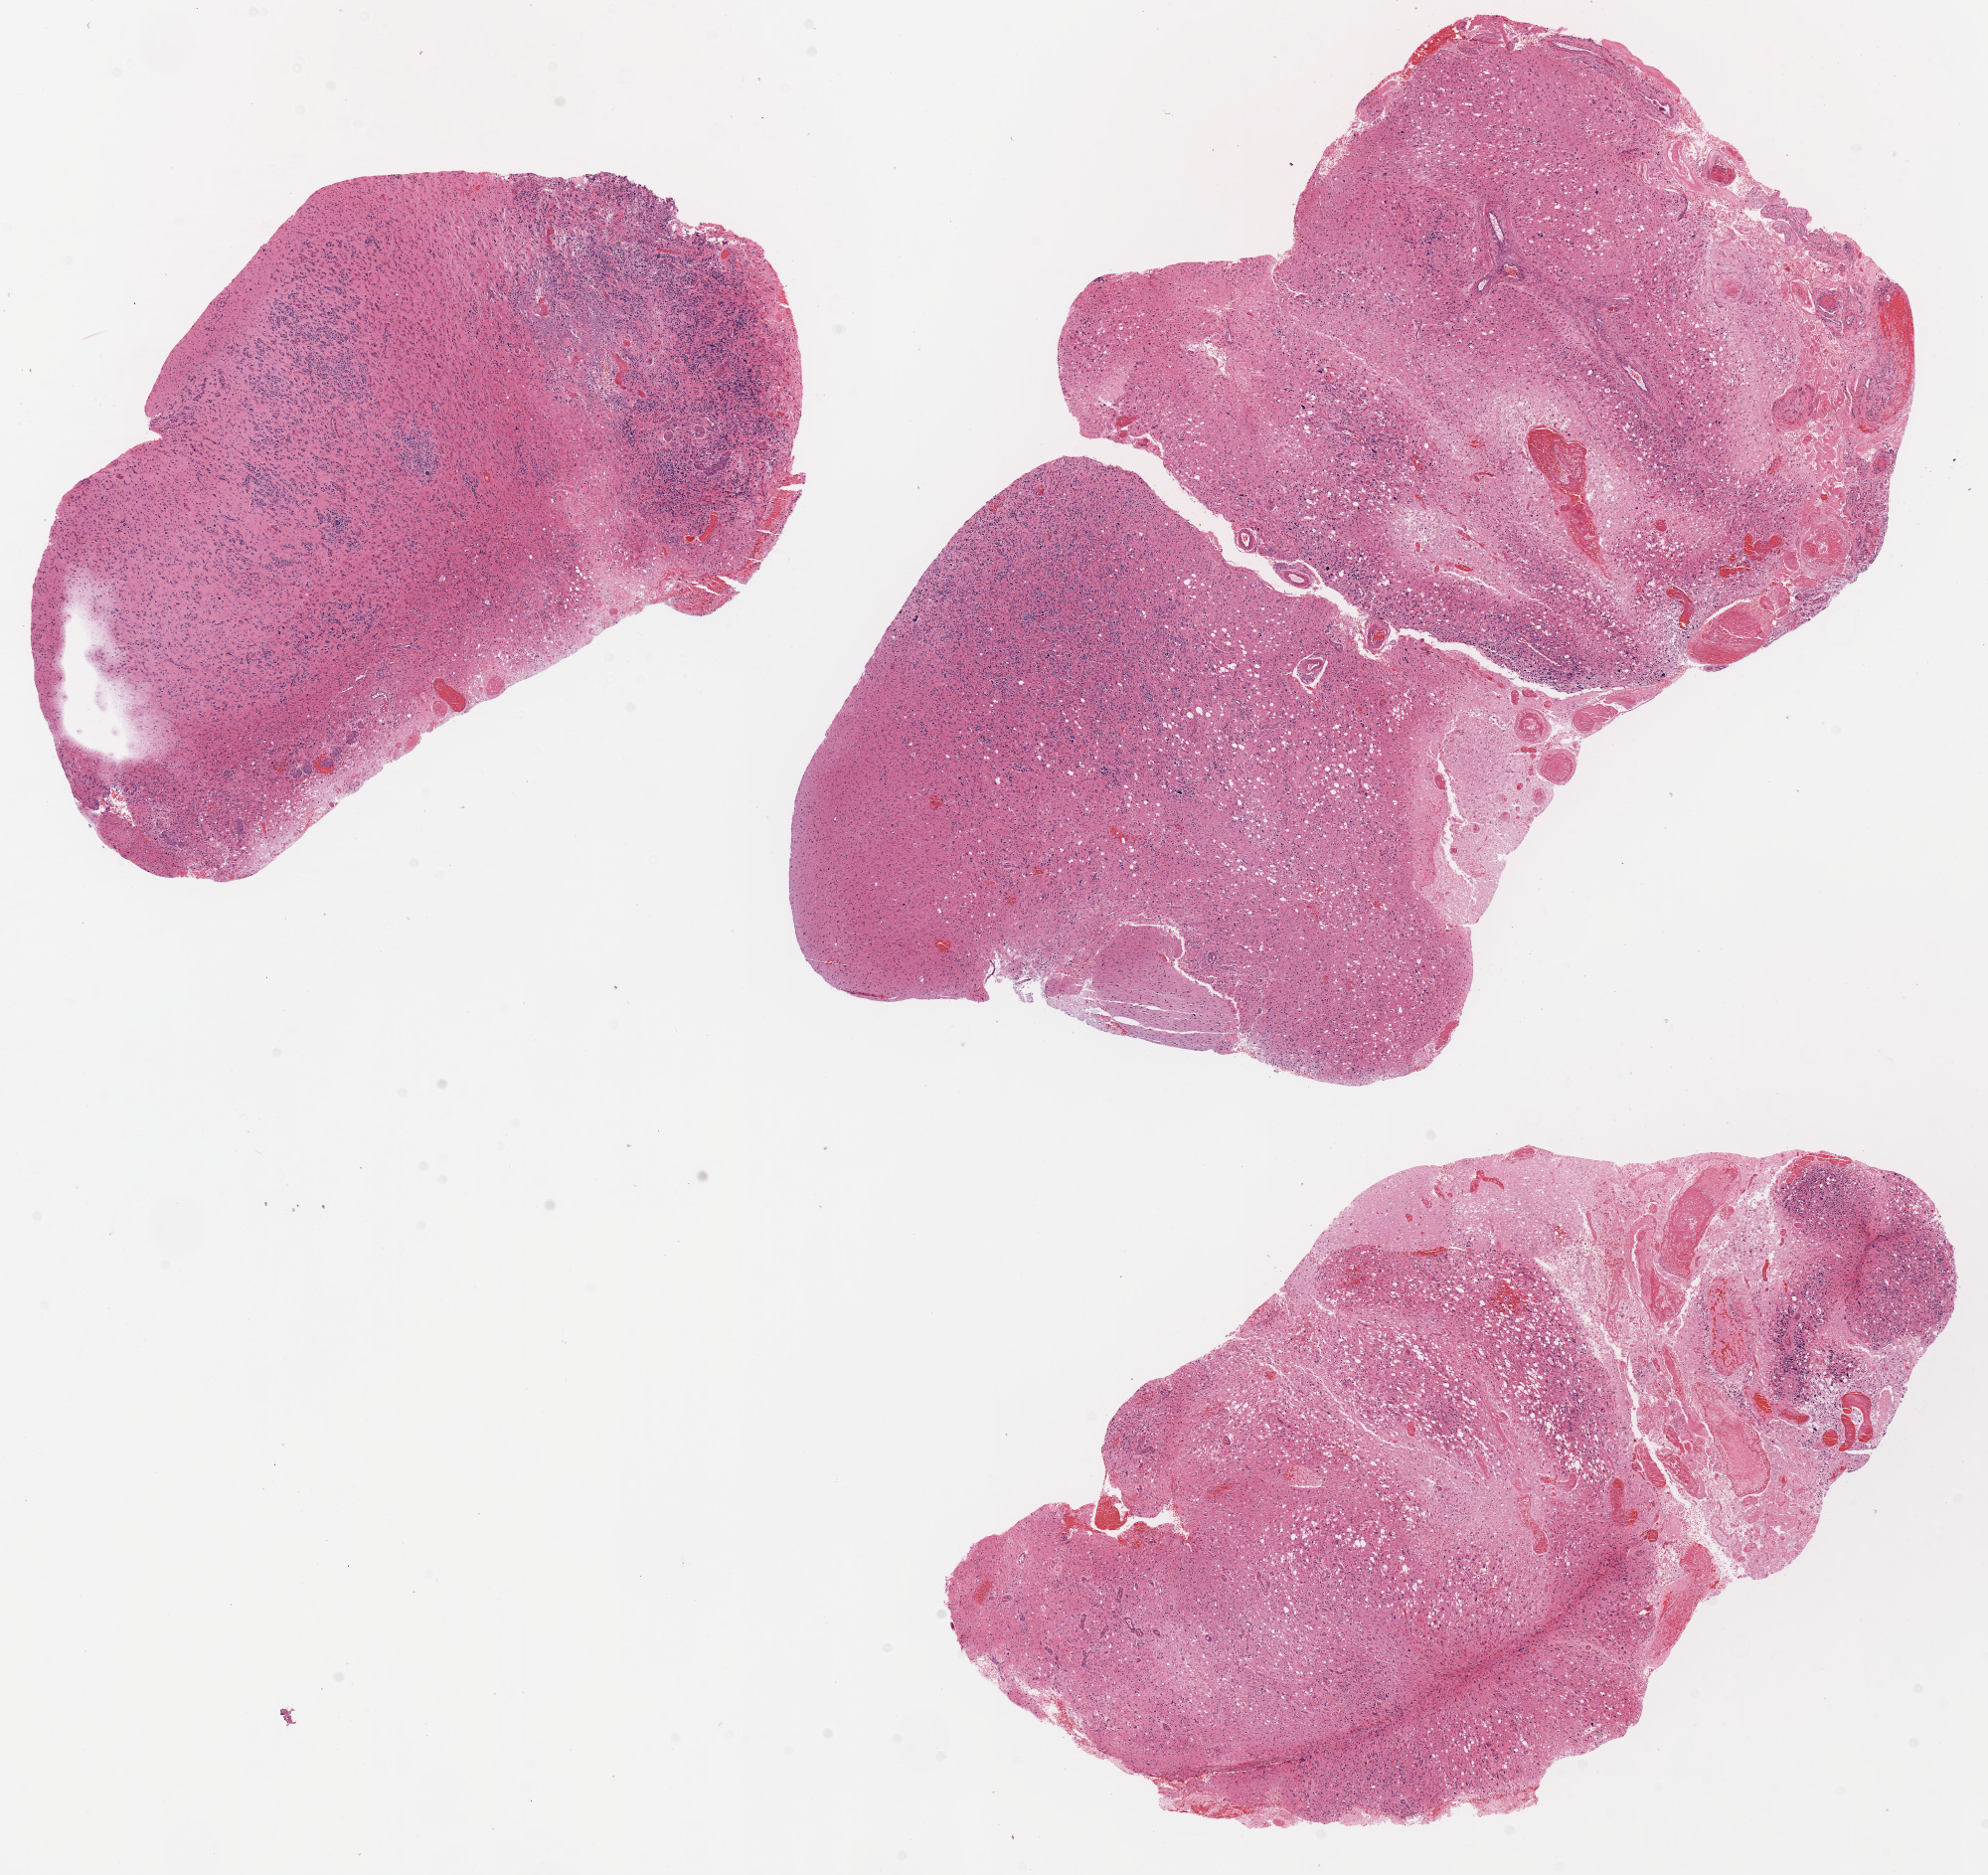
Digitized Hematoxylin and eosin (H&E) stained tissue section (whole slide), whole scanned area (about 16.0 x 15.1 mm, acquisition: 20x scan) shown as a low-resolution overview. Formalin-fixed paraffin-embedded (FFPE) diagnostic section. Brain, primary tumour sample. Female patient; age at initial diagnosis 72 years.
• histologic diagnosis: Glioblastoma